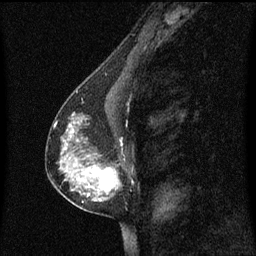
Breast MRI (dynamic contrast-enhanced), one sagittal slice; slice 35 of 60 in the series (ordered by position); dynamic contrast-enhanced series, image 2 of 3 at this slice position (ordered by acquisition); 1.5 T; TE 4.2 ms, TR 8.4 ms; 2 mm slice thickness; 256 × 256 image matrix, field of view 200 × 200 mm. Female patient, age 40 years. Case-level facts recorded for this patient, not image findings: setting: breast cancer imaged before/during neoadjuvant chemotherapy; receptor status: triple-negative.
Structures marked on this image (semi-automatic segmentation, software-assisted and operator-edited):
- analysis volume of interest (the breast-tissue region the enhancement analysis was run in; not a lesion): bounding box <60,104,127,215> (left, top, right, bottom; pixels)
- tumour enhancement mask (voxels above the 70 % enhancement threshold inside the analysis volume of interest): <70,126,121,201>